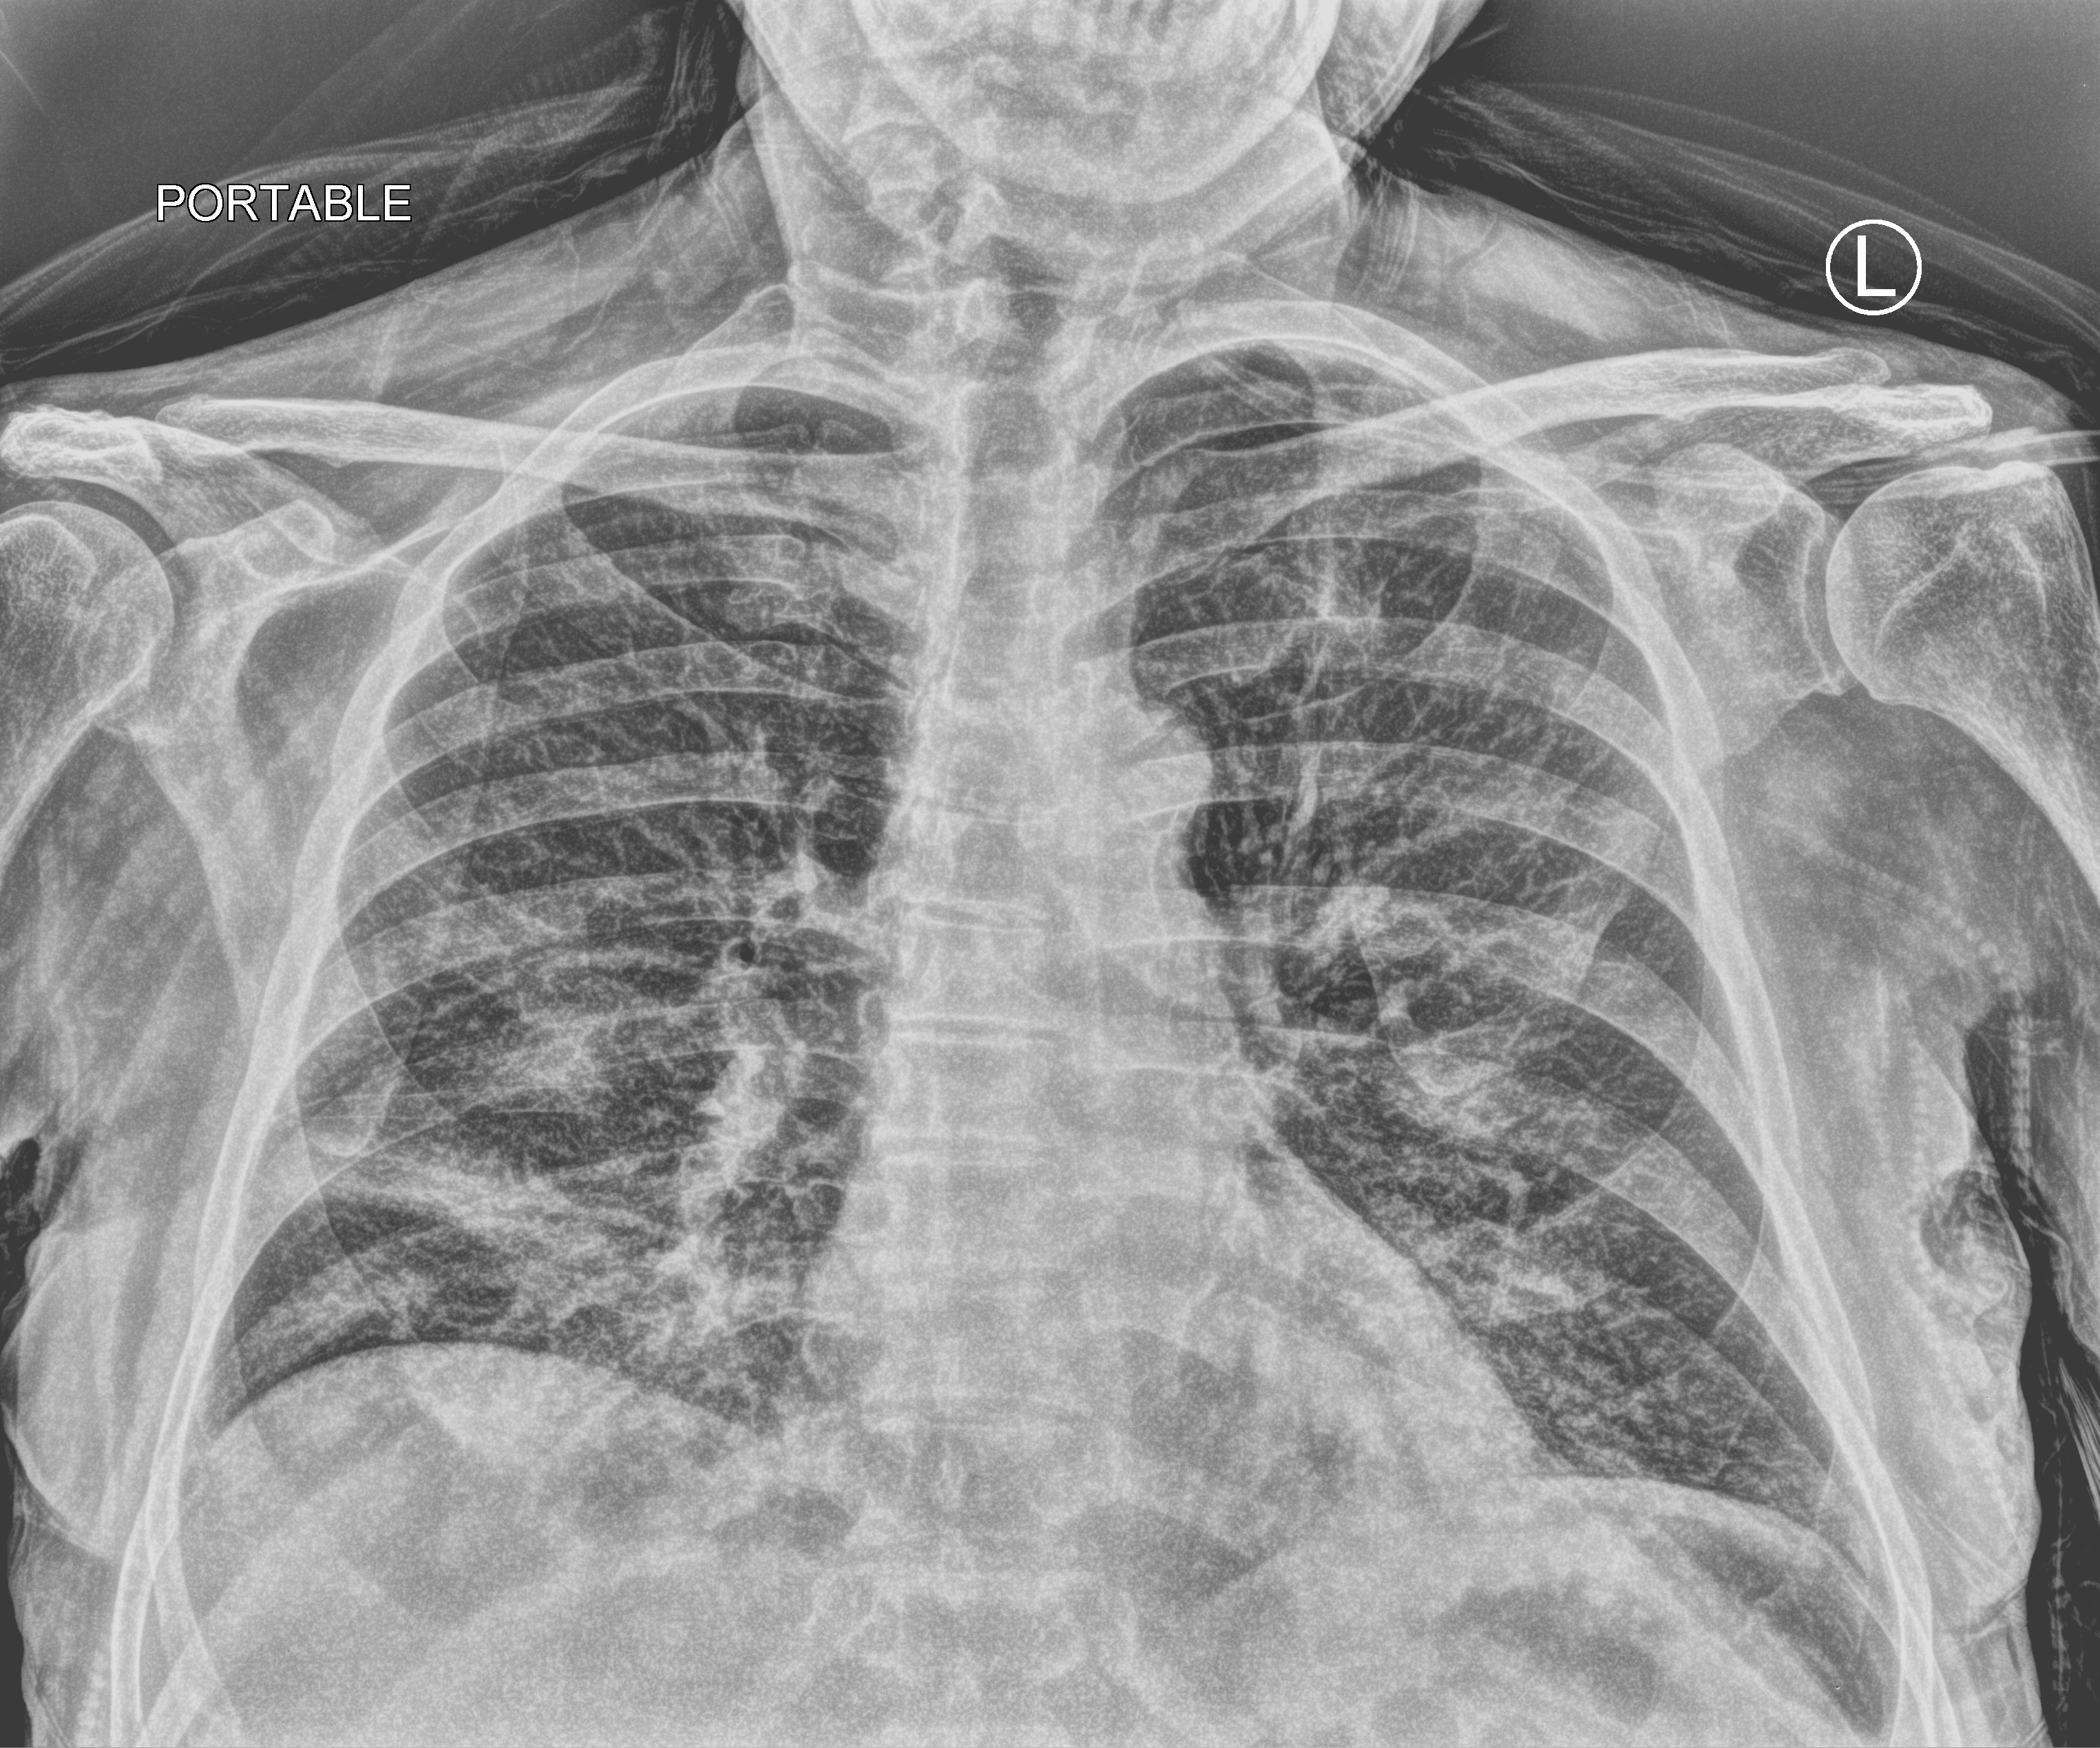
Portable chest radiograph; anteroposterior (AP) projection. Patient hospitalised with COVID-19; male, aged 60–74 years.
From the hospital-stay record, not from the radiograph (when in the stay this image was taken is not recorded): COPD (admission record): no.